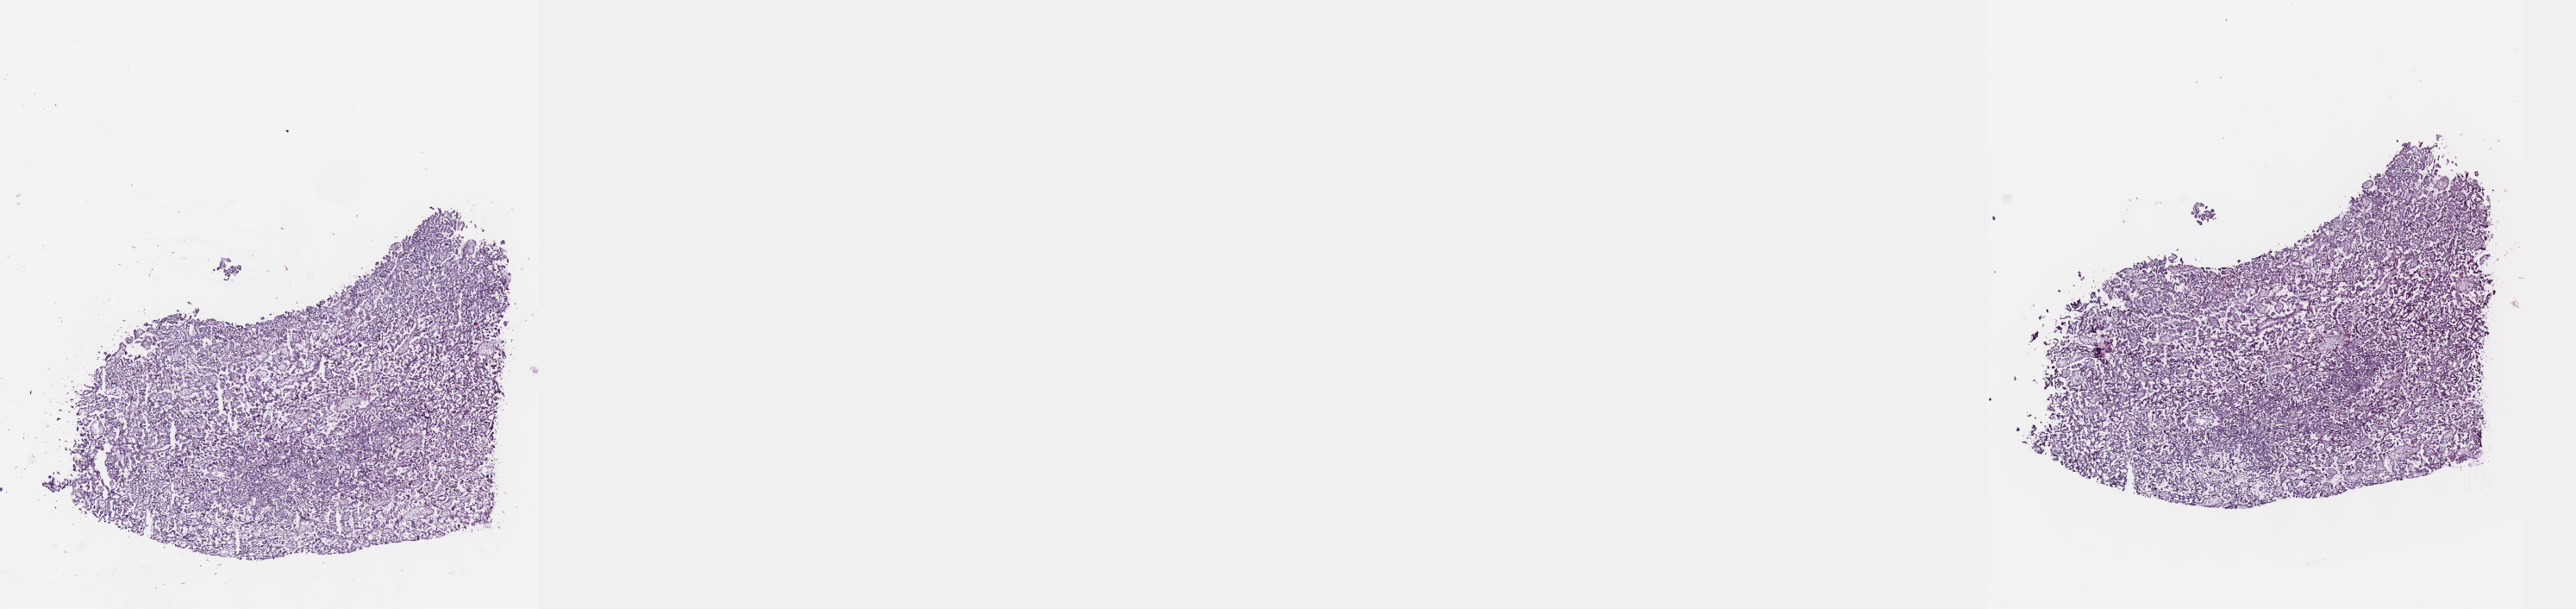
Digitized H&E-stained tissue section (whole slide), whole scanned area (about 24.1 x 5.7 mm) shown as a low-resolution overview, frozen section, sample: primary tumour, kidney. Patient: male, age at initial diagnosis 52 years. Pathologist review of this section (percent, as recorded): tumour cells 100%, tumour nuclei 80%, normal cells 0%, stromal cells 0%, necrosis 0%. Inflammatory infiltration, as recorded: lymphocyte infiltration 1%, monocyte infiltration 1%, neutrophil infiltration 0%.
AJCC pathologic stage: I (7th edition). Laterality: left. Diagnosis: Papillary adenocarcinoma, NOS.